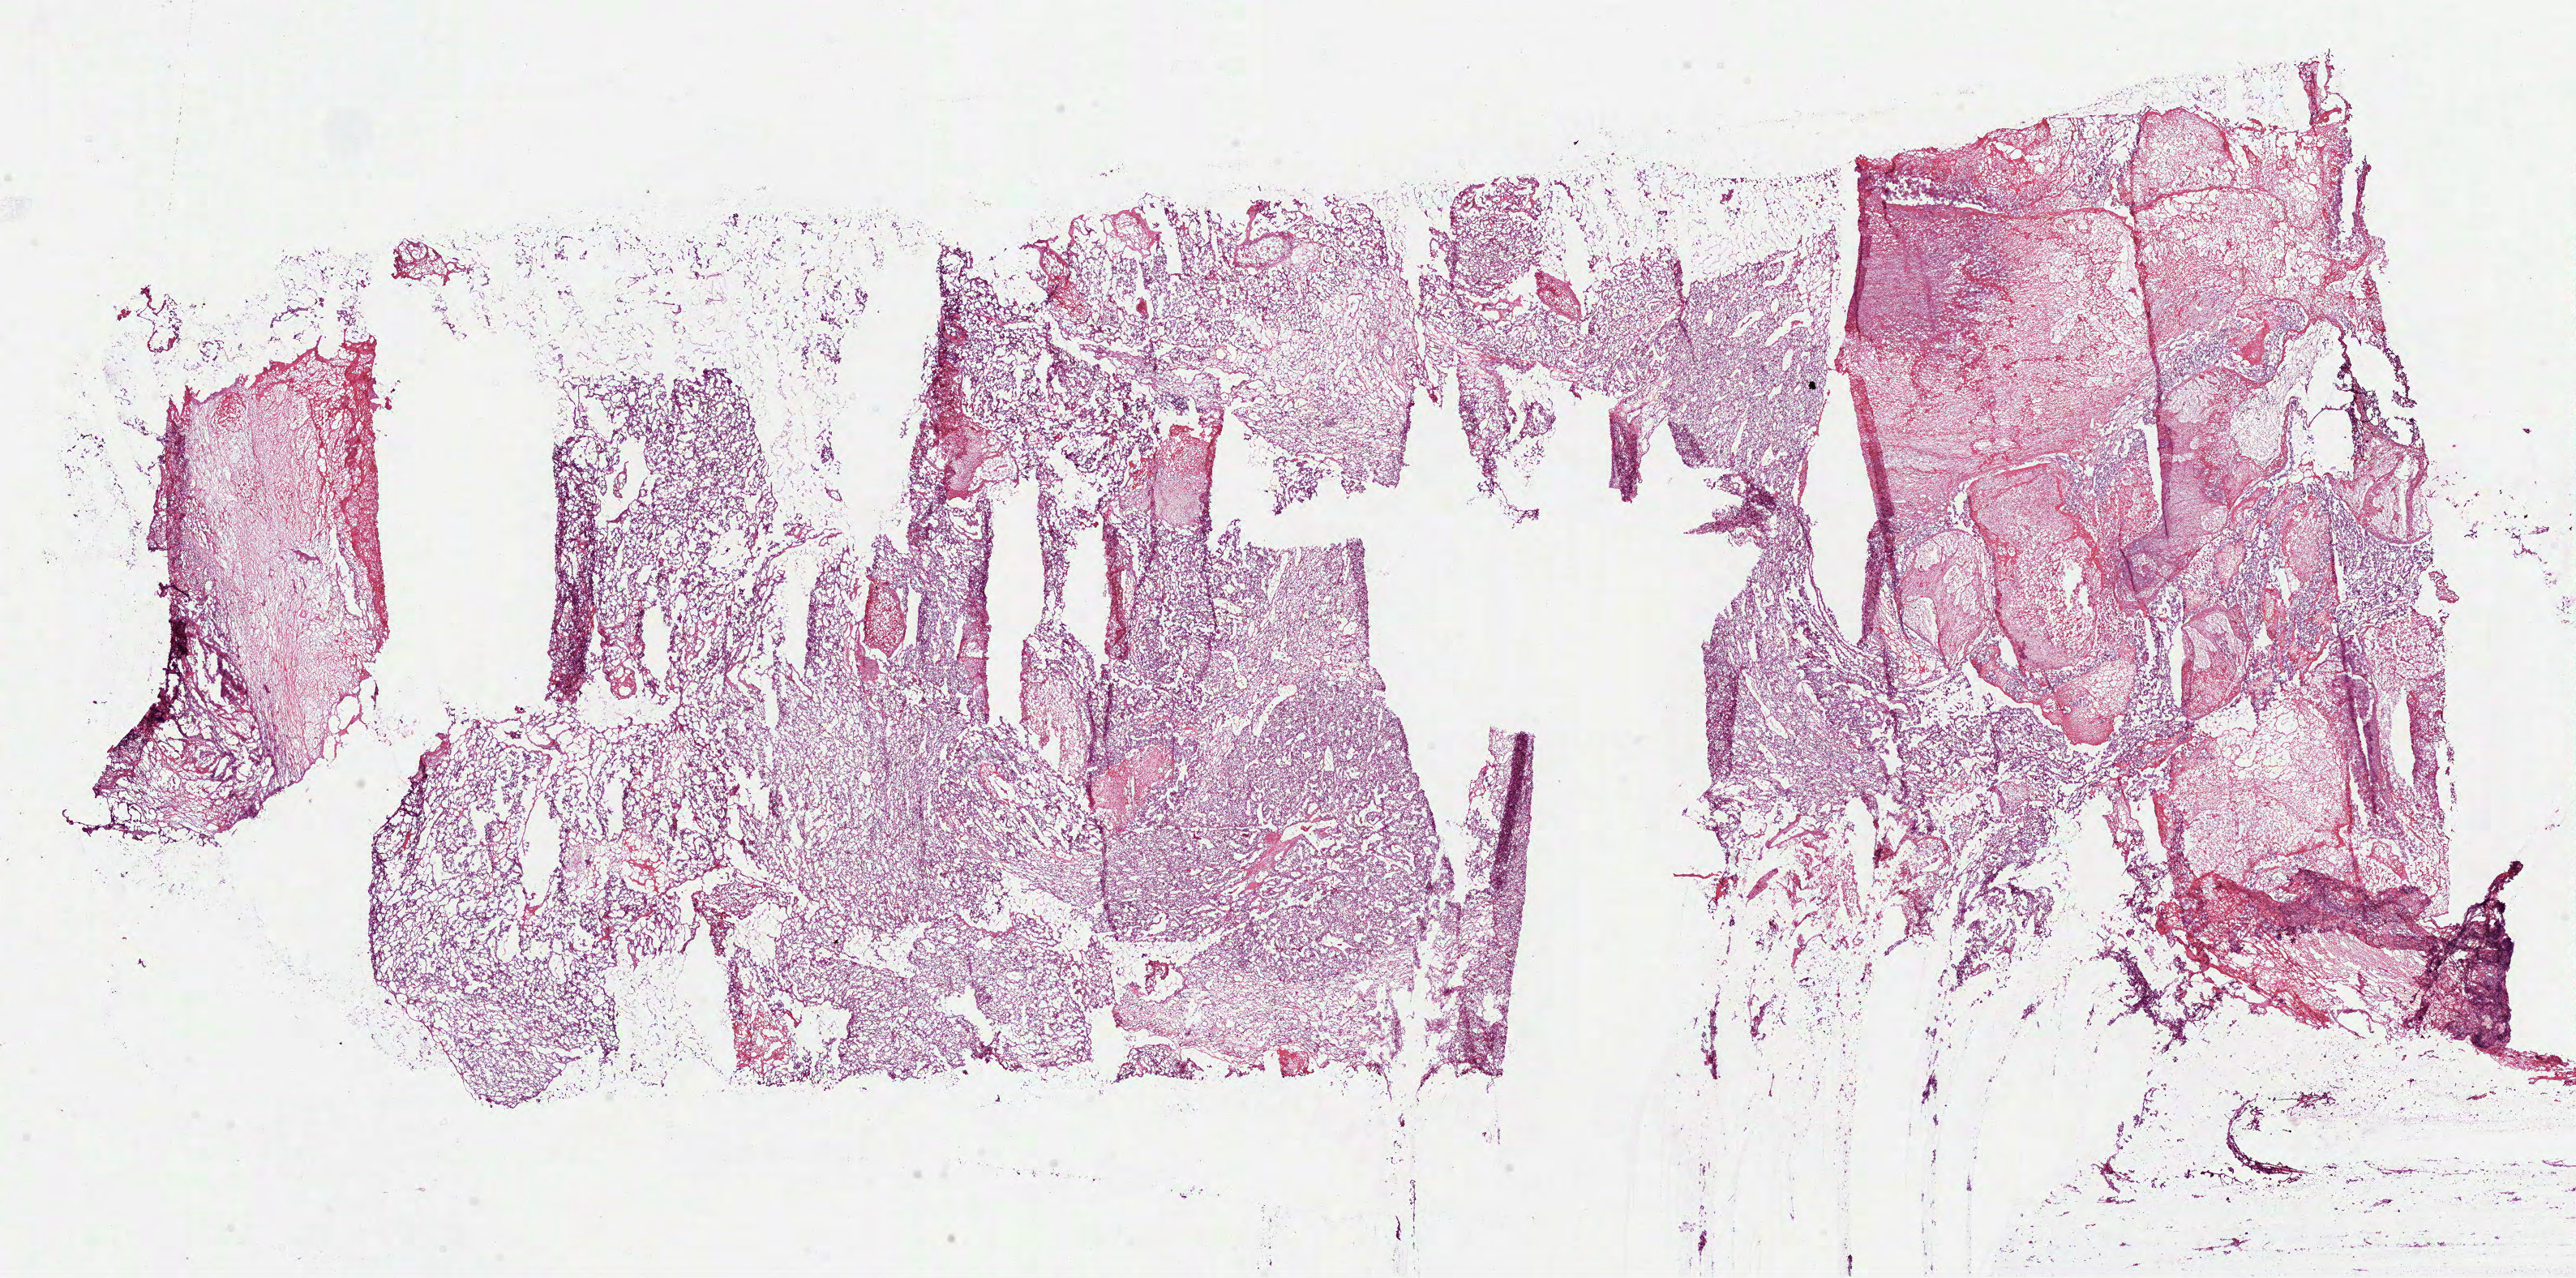
Hematoxylin and eosin (H&E) stained whole-slide image — a low-resolution overview of the entire scanned area, about 25.6 x 12.7 mm; frozen section; kidney, primary tumour sample. Female, age 54 years at initial diagnosis. Histologic grade: G4 (undifferentiated). Slide review estimates, as recorded: tumour cells 75%, tumour nuclei 75%, normal cells 0%, stromal cells 25%, necrosis 0%.
* AJCC pathologic stage: IV (6th edition)
* histologic diagnosis: Clear cell adenocarcinoma, NOS